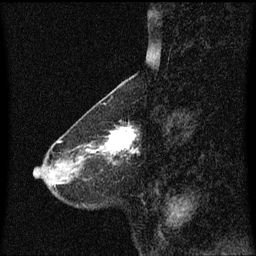
Breast MRI (dynamic contrast-enhanced), one sagittal slice. Position 22 of 60 along the scan axis. Dynamic contrast-enhanced series, image 2 of 3 at this slice position (ordered by acquisition). 1.5 T. TE 4.2 ms, TR 8.4 ms. 256 × 256 image matrix, field of view 200 × 200 mm. Patient: female, 58 years.
Outlined on this slice (semi-automatically segmented with operator editing):
- analysis volume of interest (the breast-tissue region the enhancement analysis was run in; not a lesion): bounding box <100,125,139,160> (left, top, right, bottom; pixels)
- tumour enhancement mask (voxels above the 70 % enhancement threshold inside the analysis volume of interest): <100,127,137,154>